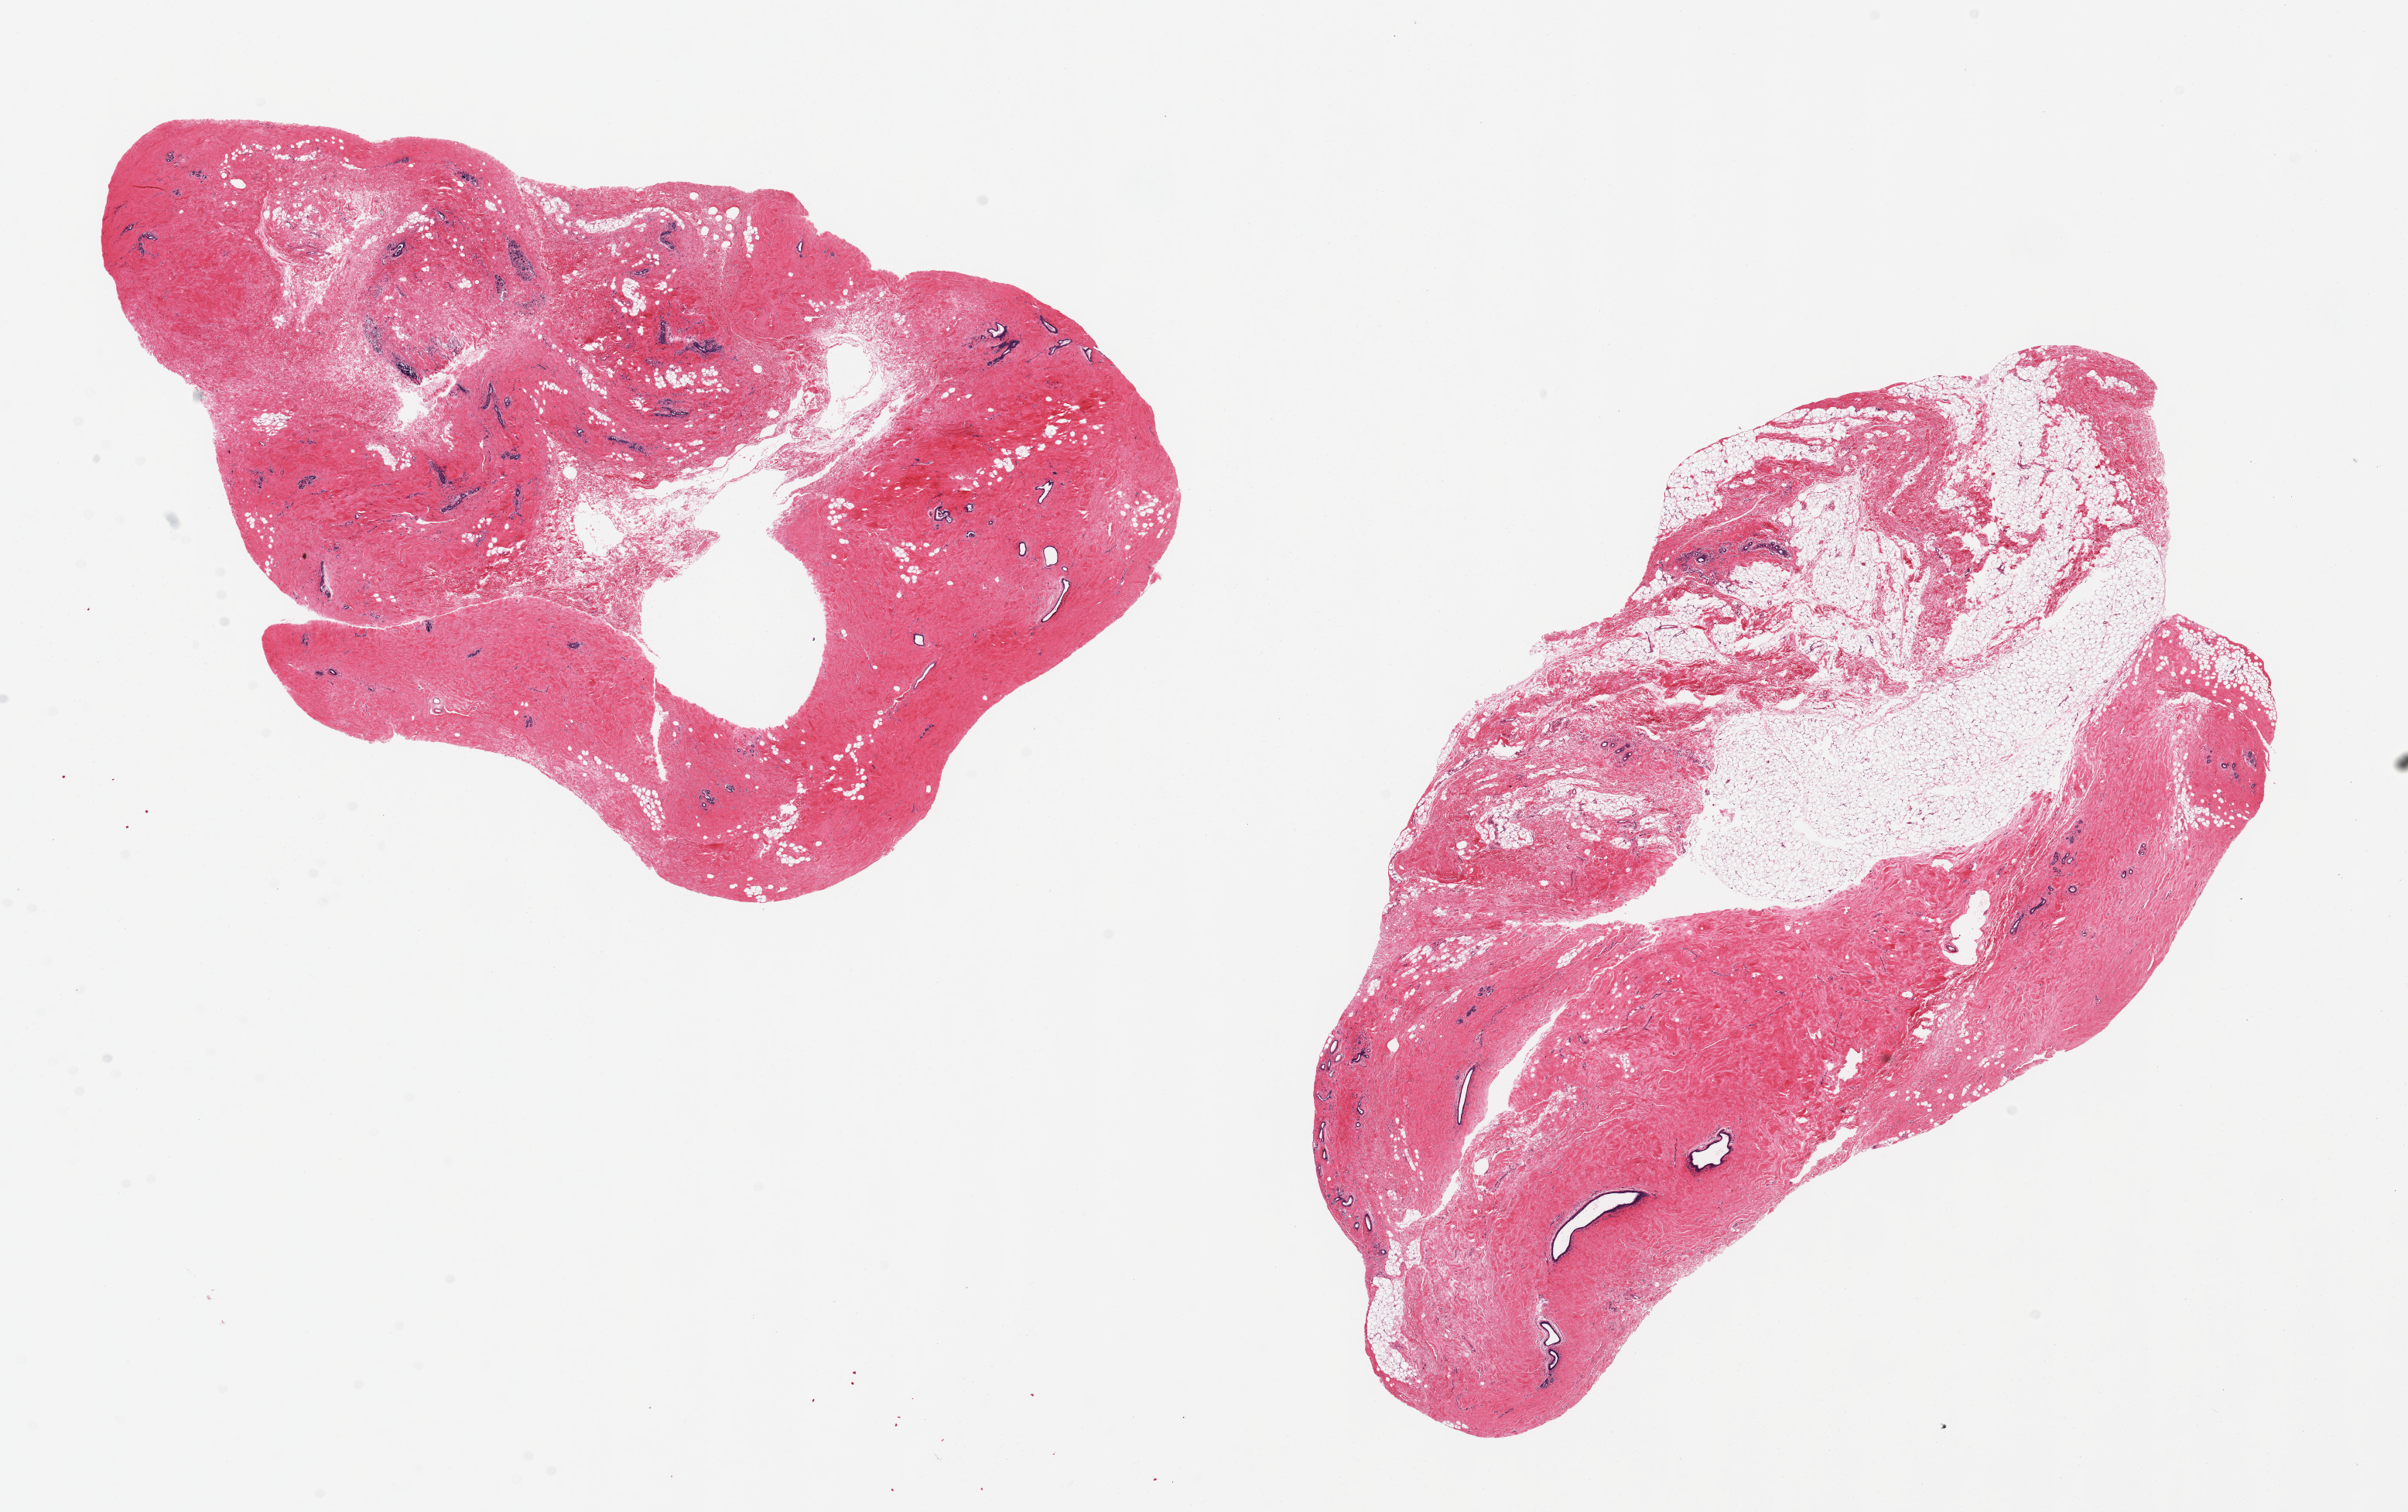
H&E whole-slide image, shown as a low-resolution overview of the whole scanned area (about 24.6 x 15.5 mm), PAXgene-fixed paraffin-embedded (PFPE) section, target tissue: breast, donor tissue sample.
• pathologist's review note for this sample: 2 pieces 13x6 & 10x7 mm; atrophic, fibrotic some residual lobules; ~25% adipose in 1 piece